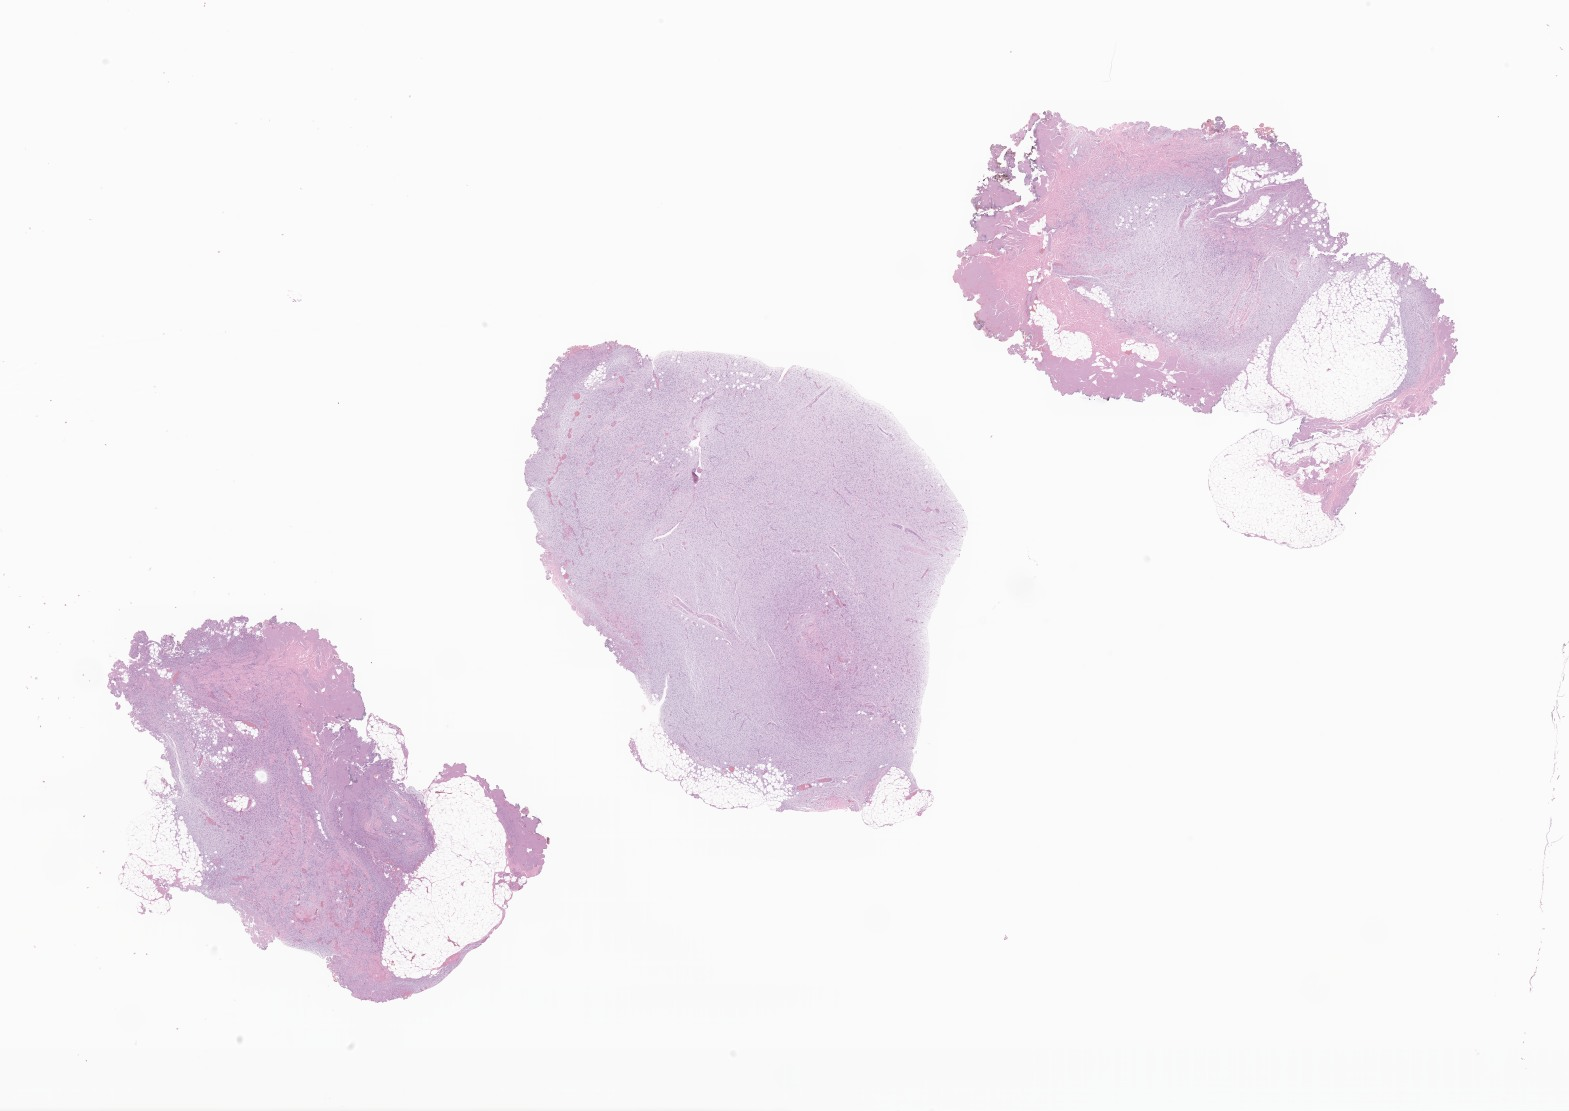
Haematoxylin and eosin whole-slide image of tumor tissue from the lymph node, low-resolution overview of the scanned area, about 26.5 x 18.7 mm. FFPE section. Female patient, age 216 months (18 years).
Diagnosis (ICD-O-3 morphology term): Dermatofibrosarcoma protuberans, fibrosarcomatous.